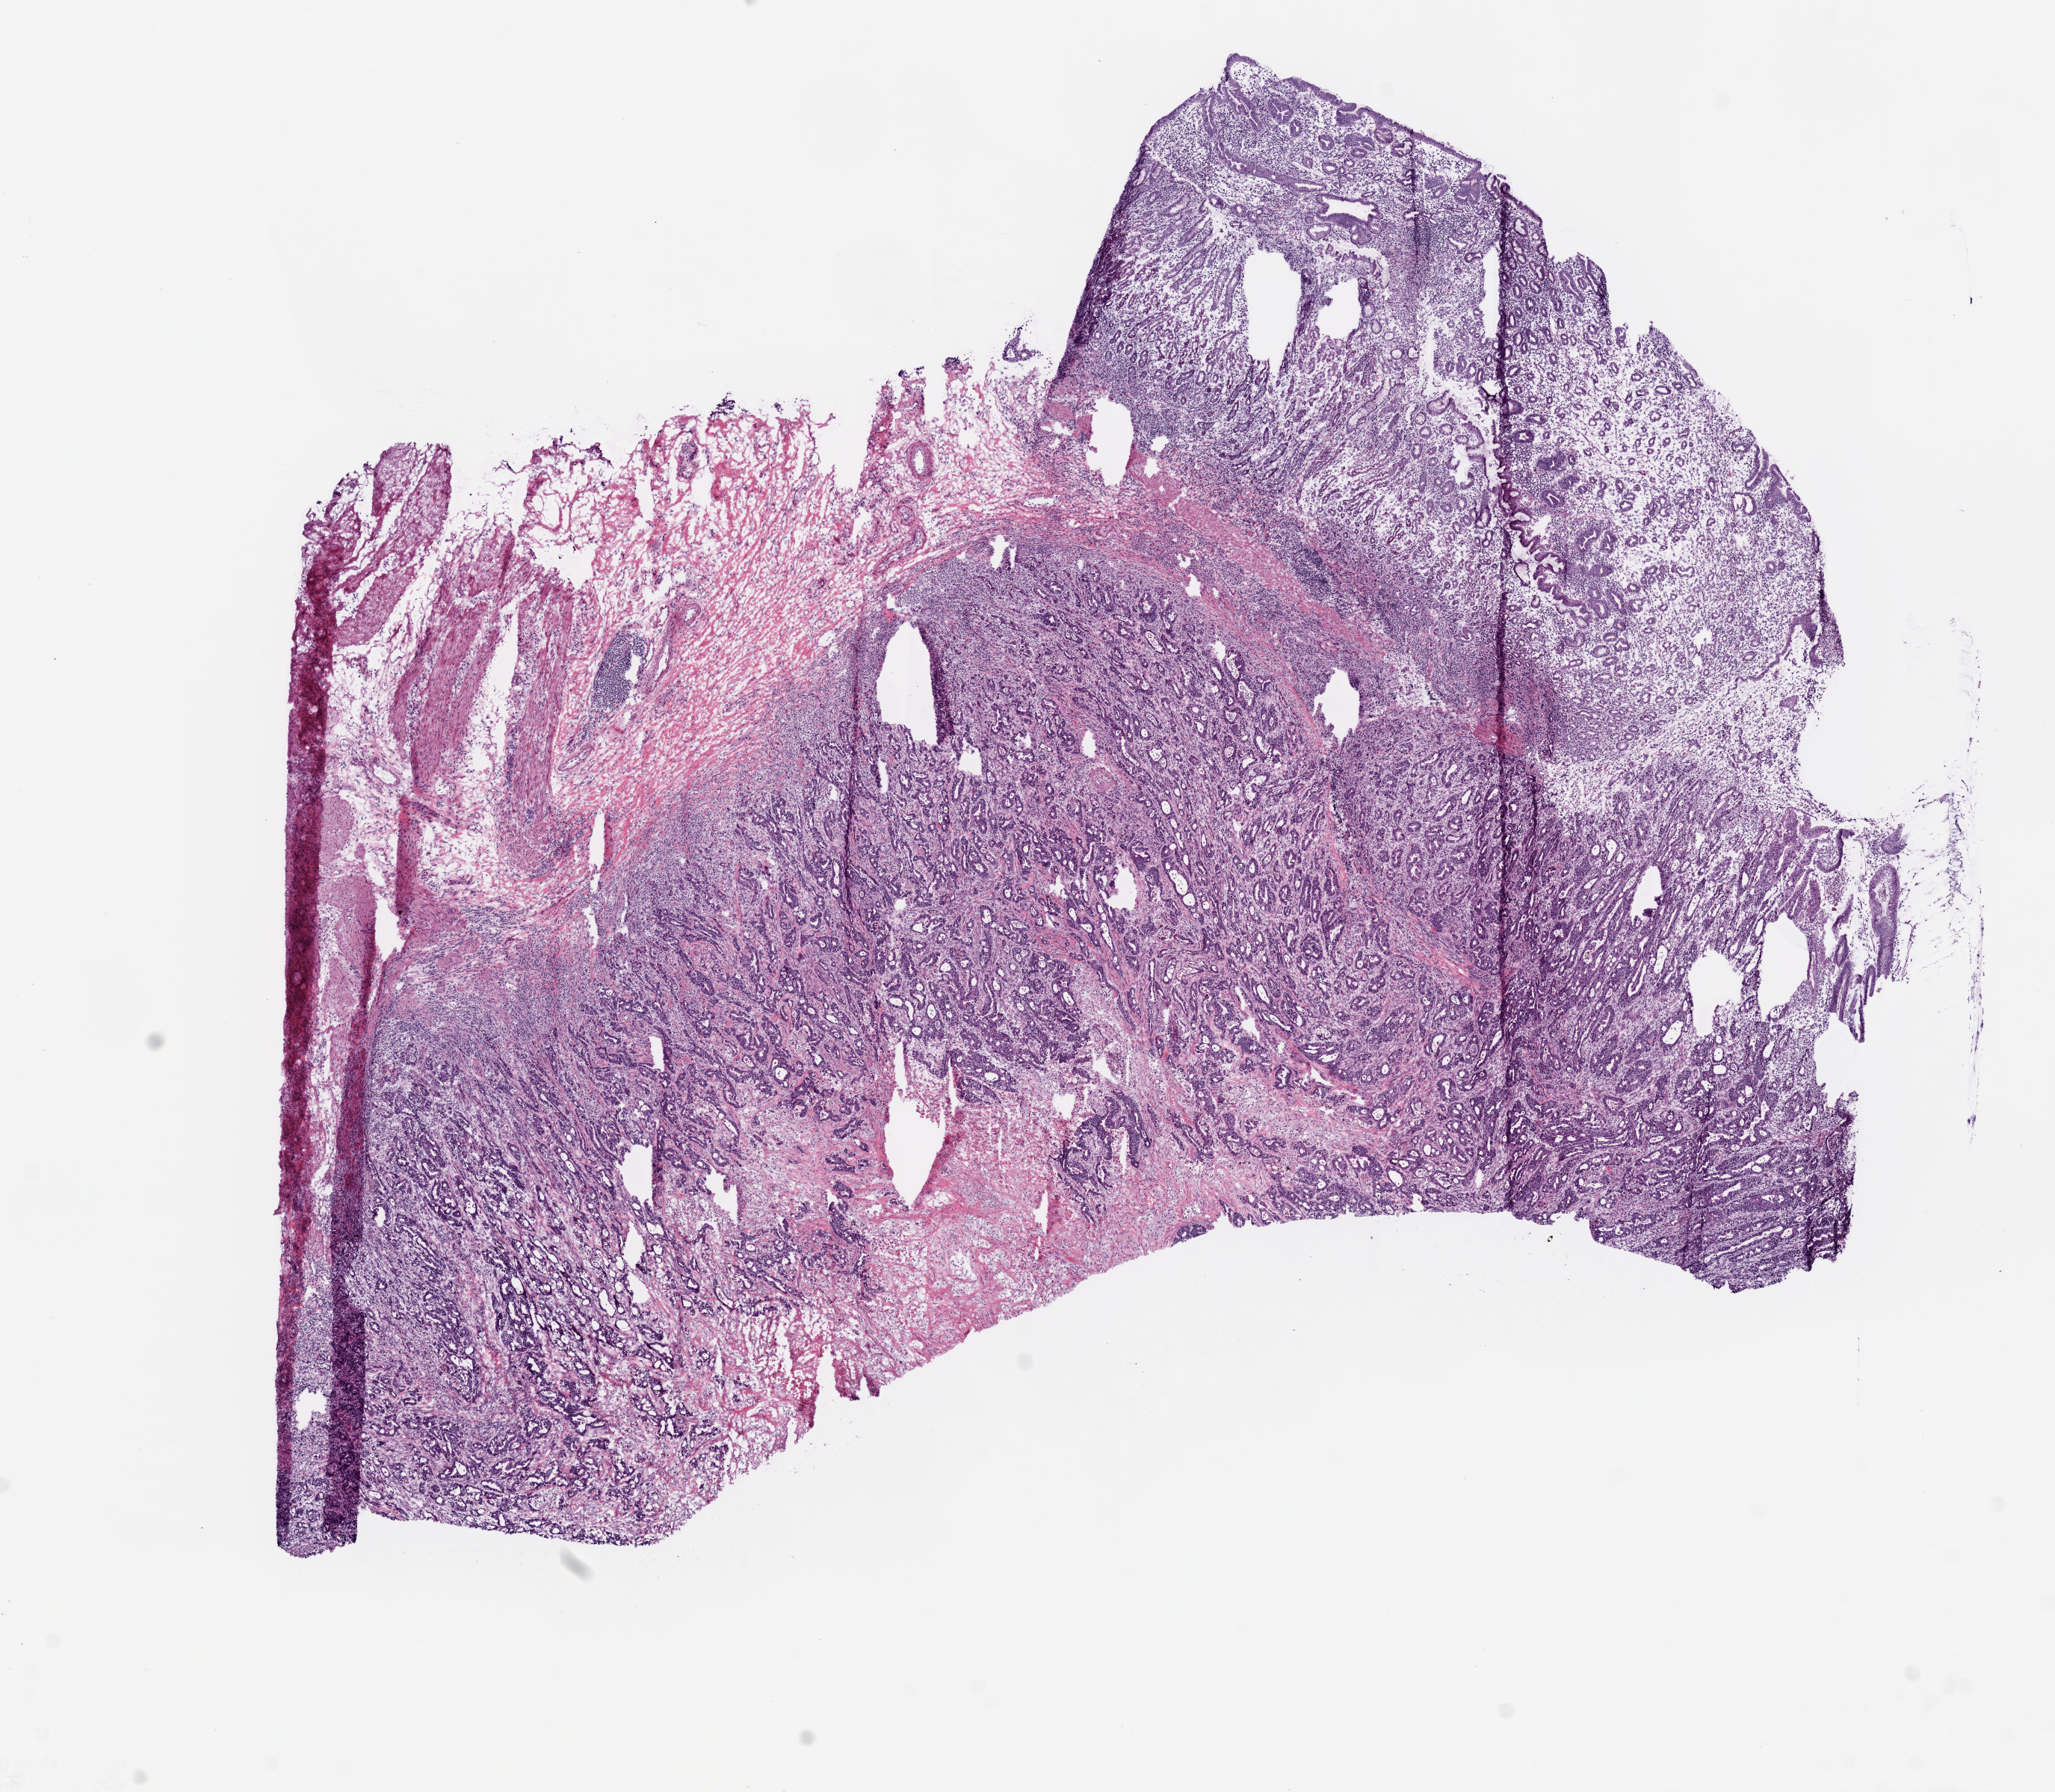
Hematoxylin and eosin (H&E) stained whole-slide image — shown as a low-resolution overview of the whole scanned area (about 11.0 x 9.6 mm). Frozen section. Sample: primary tumour, stomach. Male patient; age at initial diagnosis 83 years.
Pathologic diagnosis: Adenocarcinoma, intestinal type.